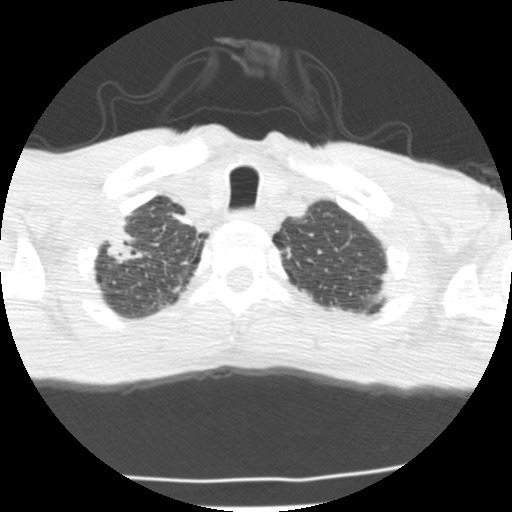
Low-dose screening chest CT, one axial slice; slice 191 of 214 in the series (ordered by position); reconstruction kernel STANDARD; lung window (W 1500 / L -600 HU); 512 × 512 image matrix, field of view 283 × 283 mm.
Outlined on this slice (expert manual segmentation):
- lesion 1 (tumor, upper lobe of right lung): bounding box [x1, y1, x2, y2] px = [107, 222, 143, 264]